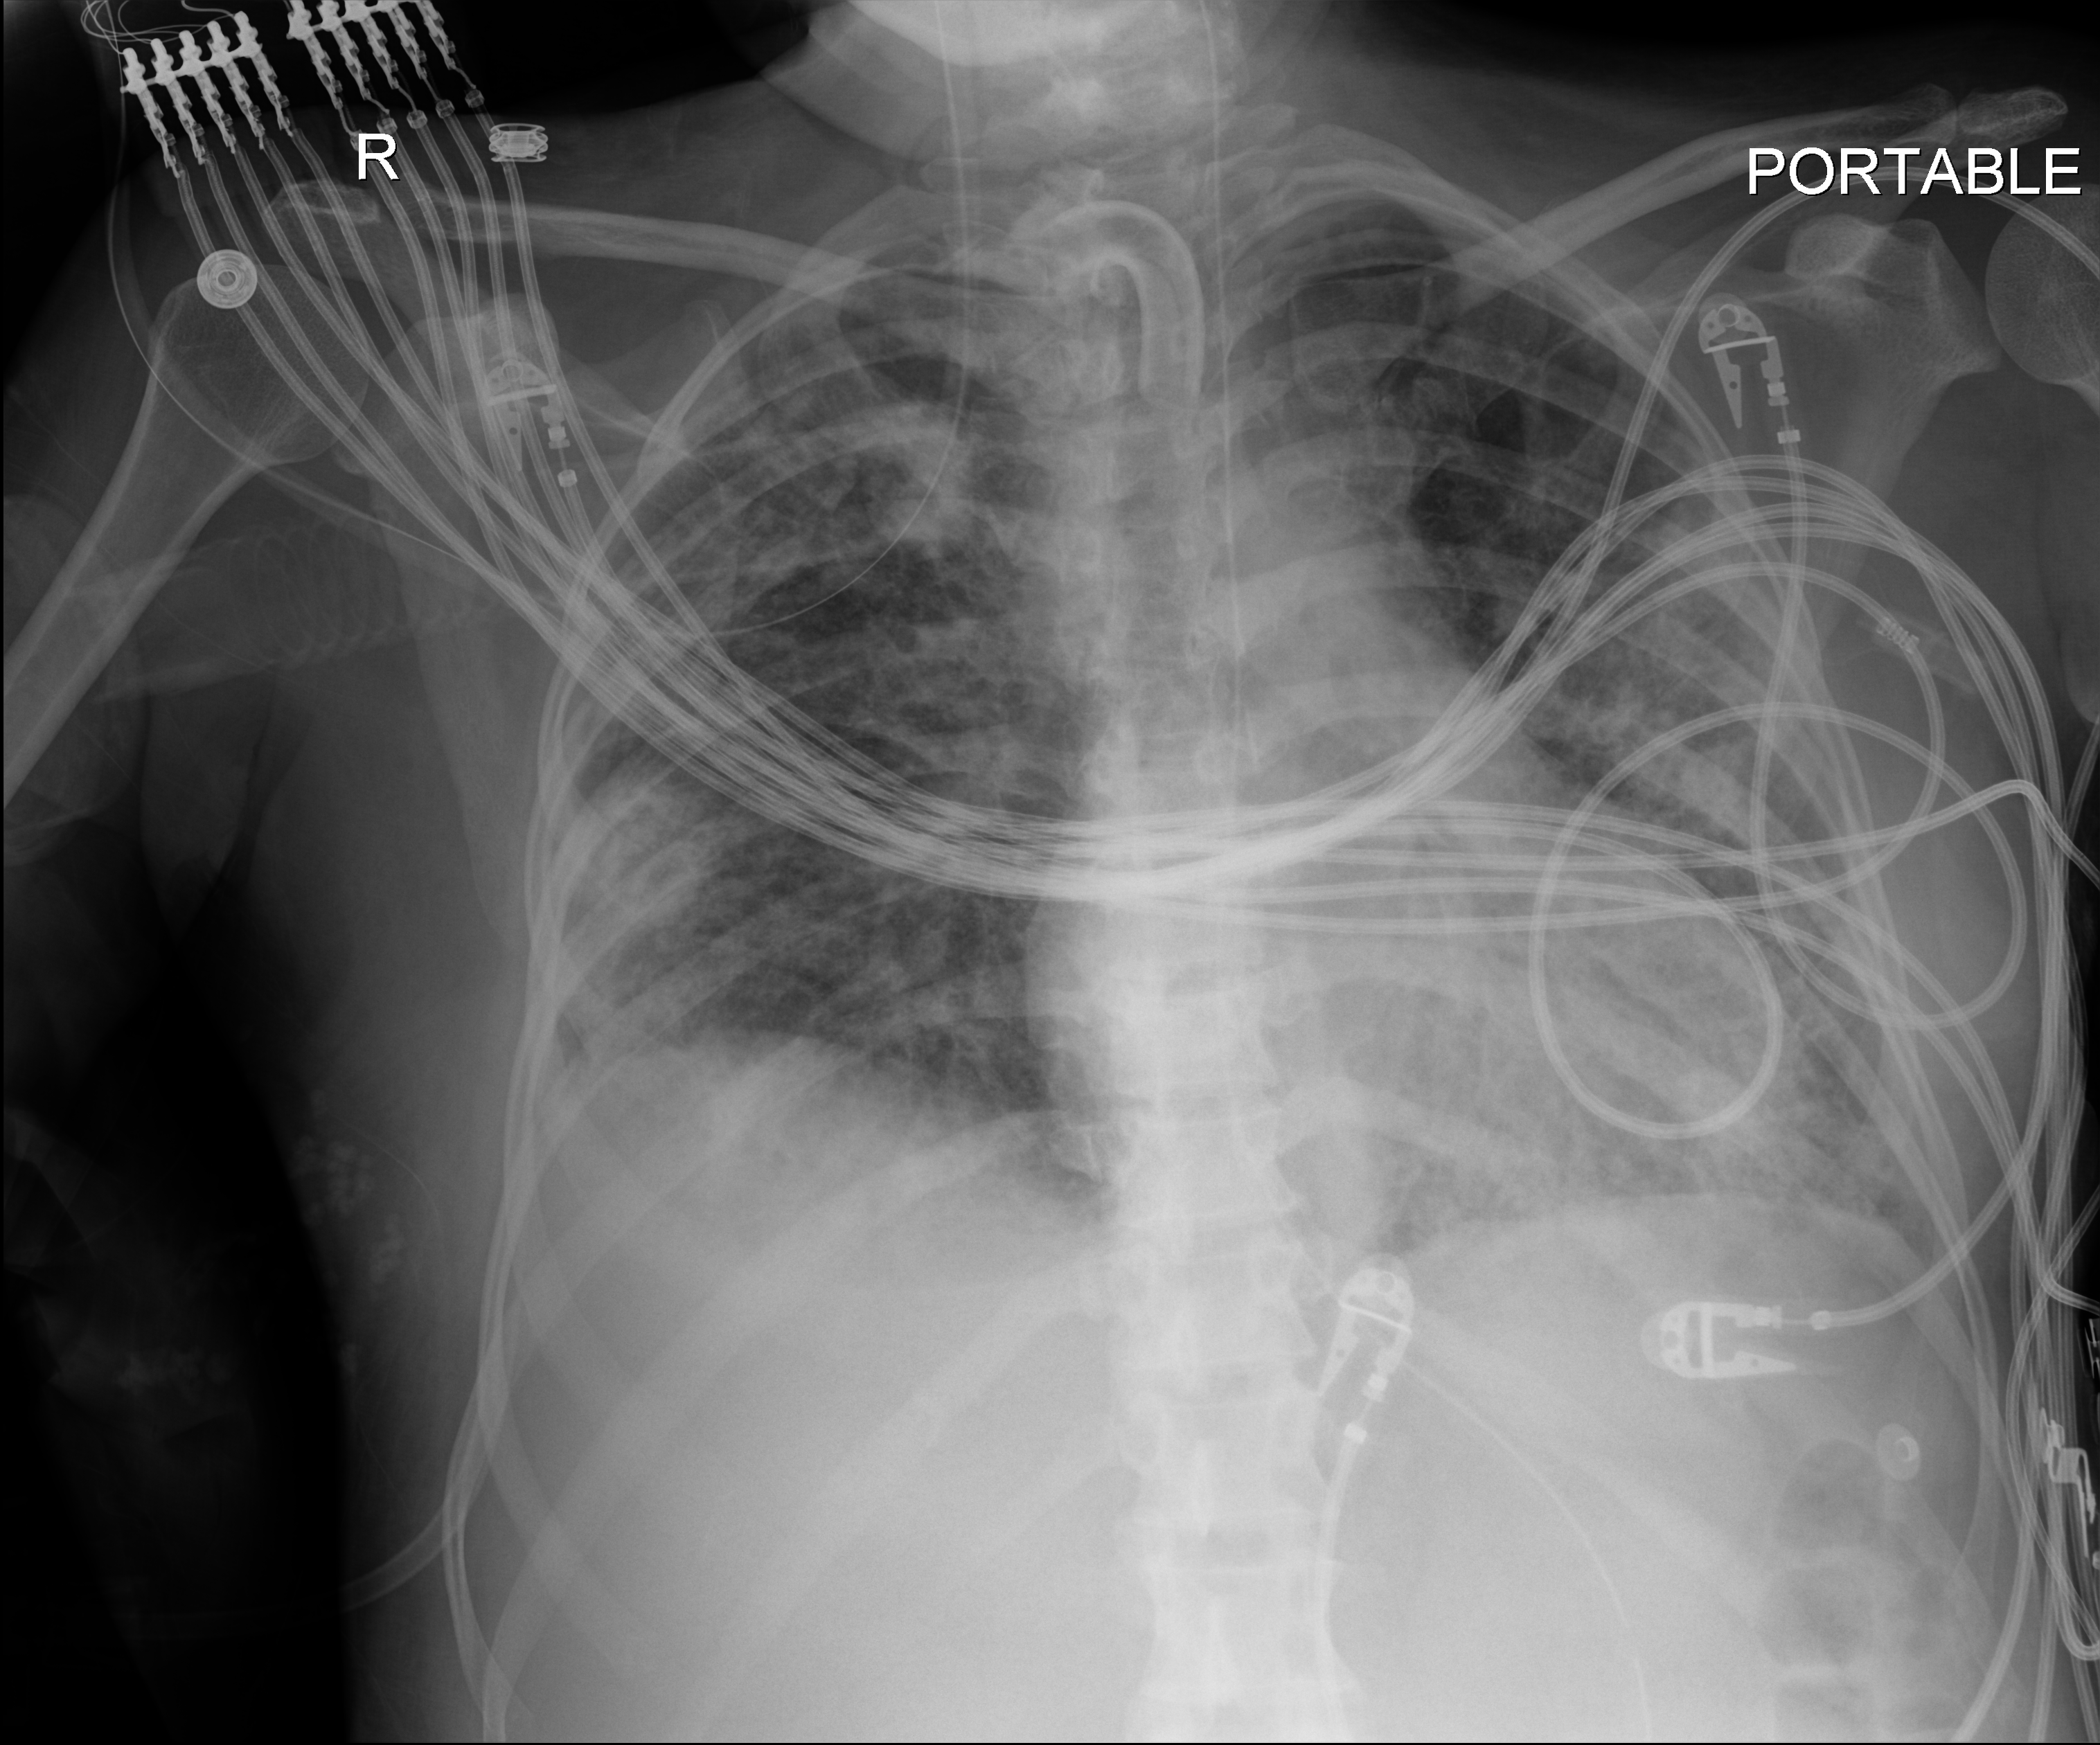
Portable chest radiograph, anteroposterior (AP) projection. Female patient hospitalised with COVID-19, age 18–59 years.
From the hospital-stay record, not from the radiograph (when in the stay this image was taken is not recorded):
- admitted to intensive care during this hospital stay: yes